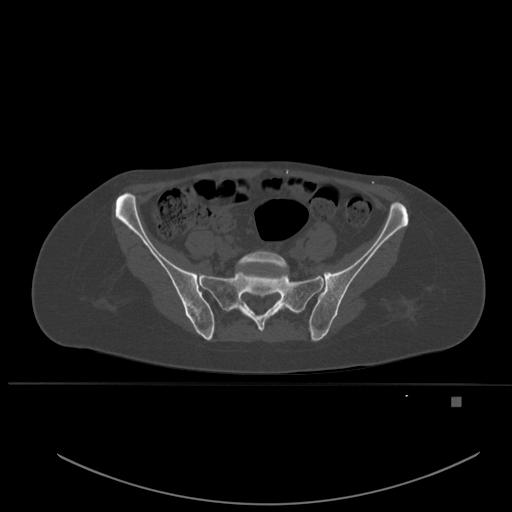
CT including the spine, one axial slice; position 140 of 651 along the scan axis; bone window (W 1800 / L 400 HU); 512 × 512 image matrix. Female patient, age 49 years. From the clinical record (not read from this slice): primary cancer: breast; vertebrae with lytic lesions (as recorded): L3, T12, L4.
Annotated regions visible in this slice (semi-automatically segmented with operator editing):
- L5 vertebra: box from (x=236, y=251) to (x=288, y=309) px